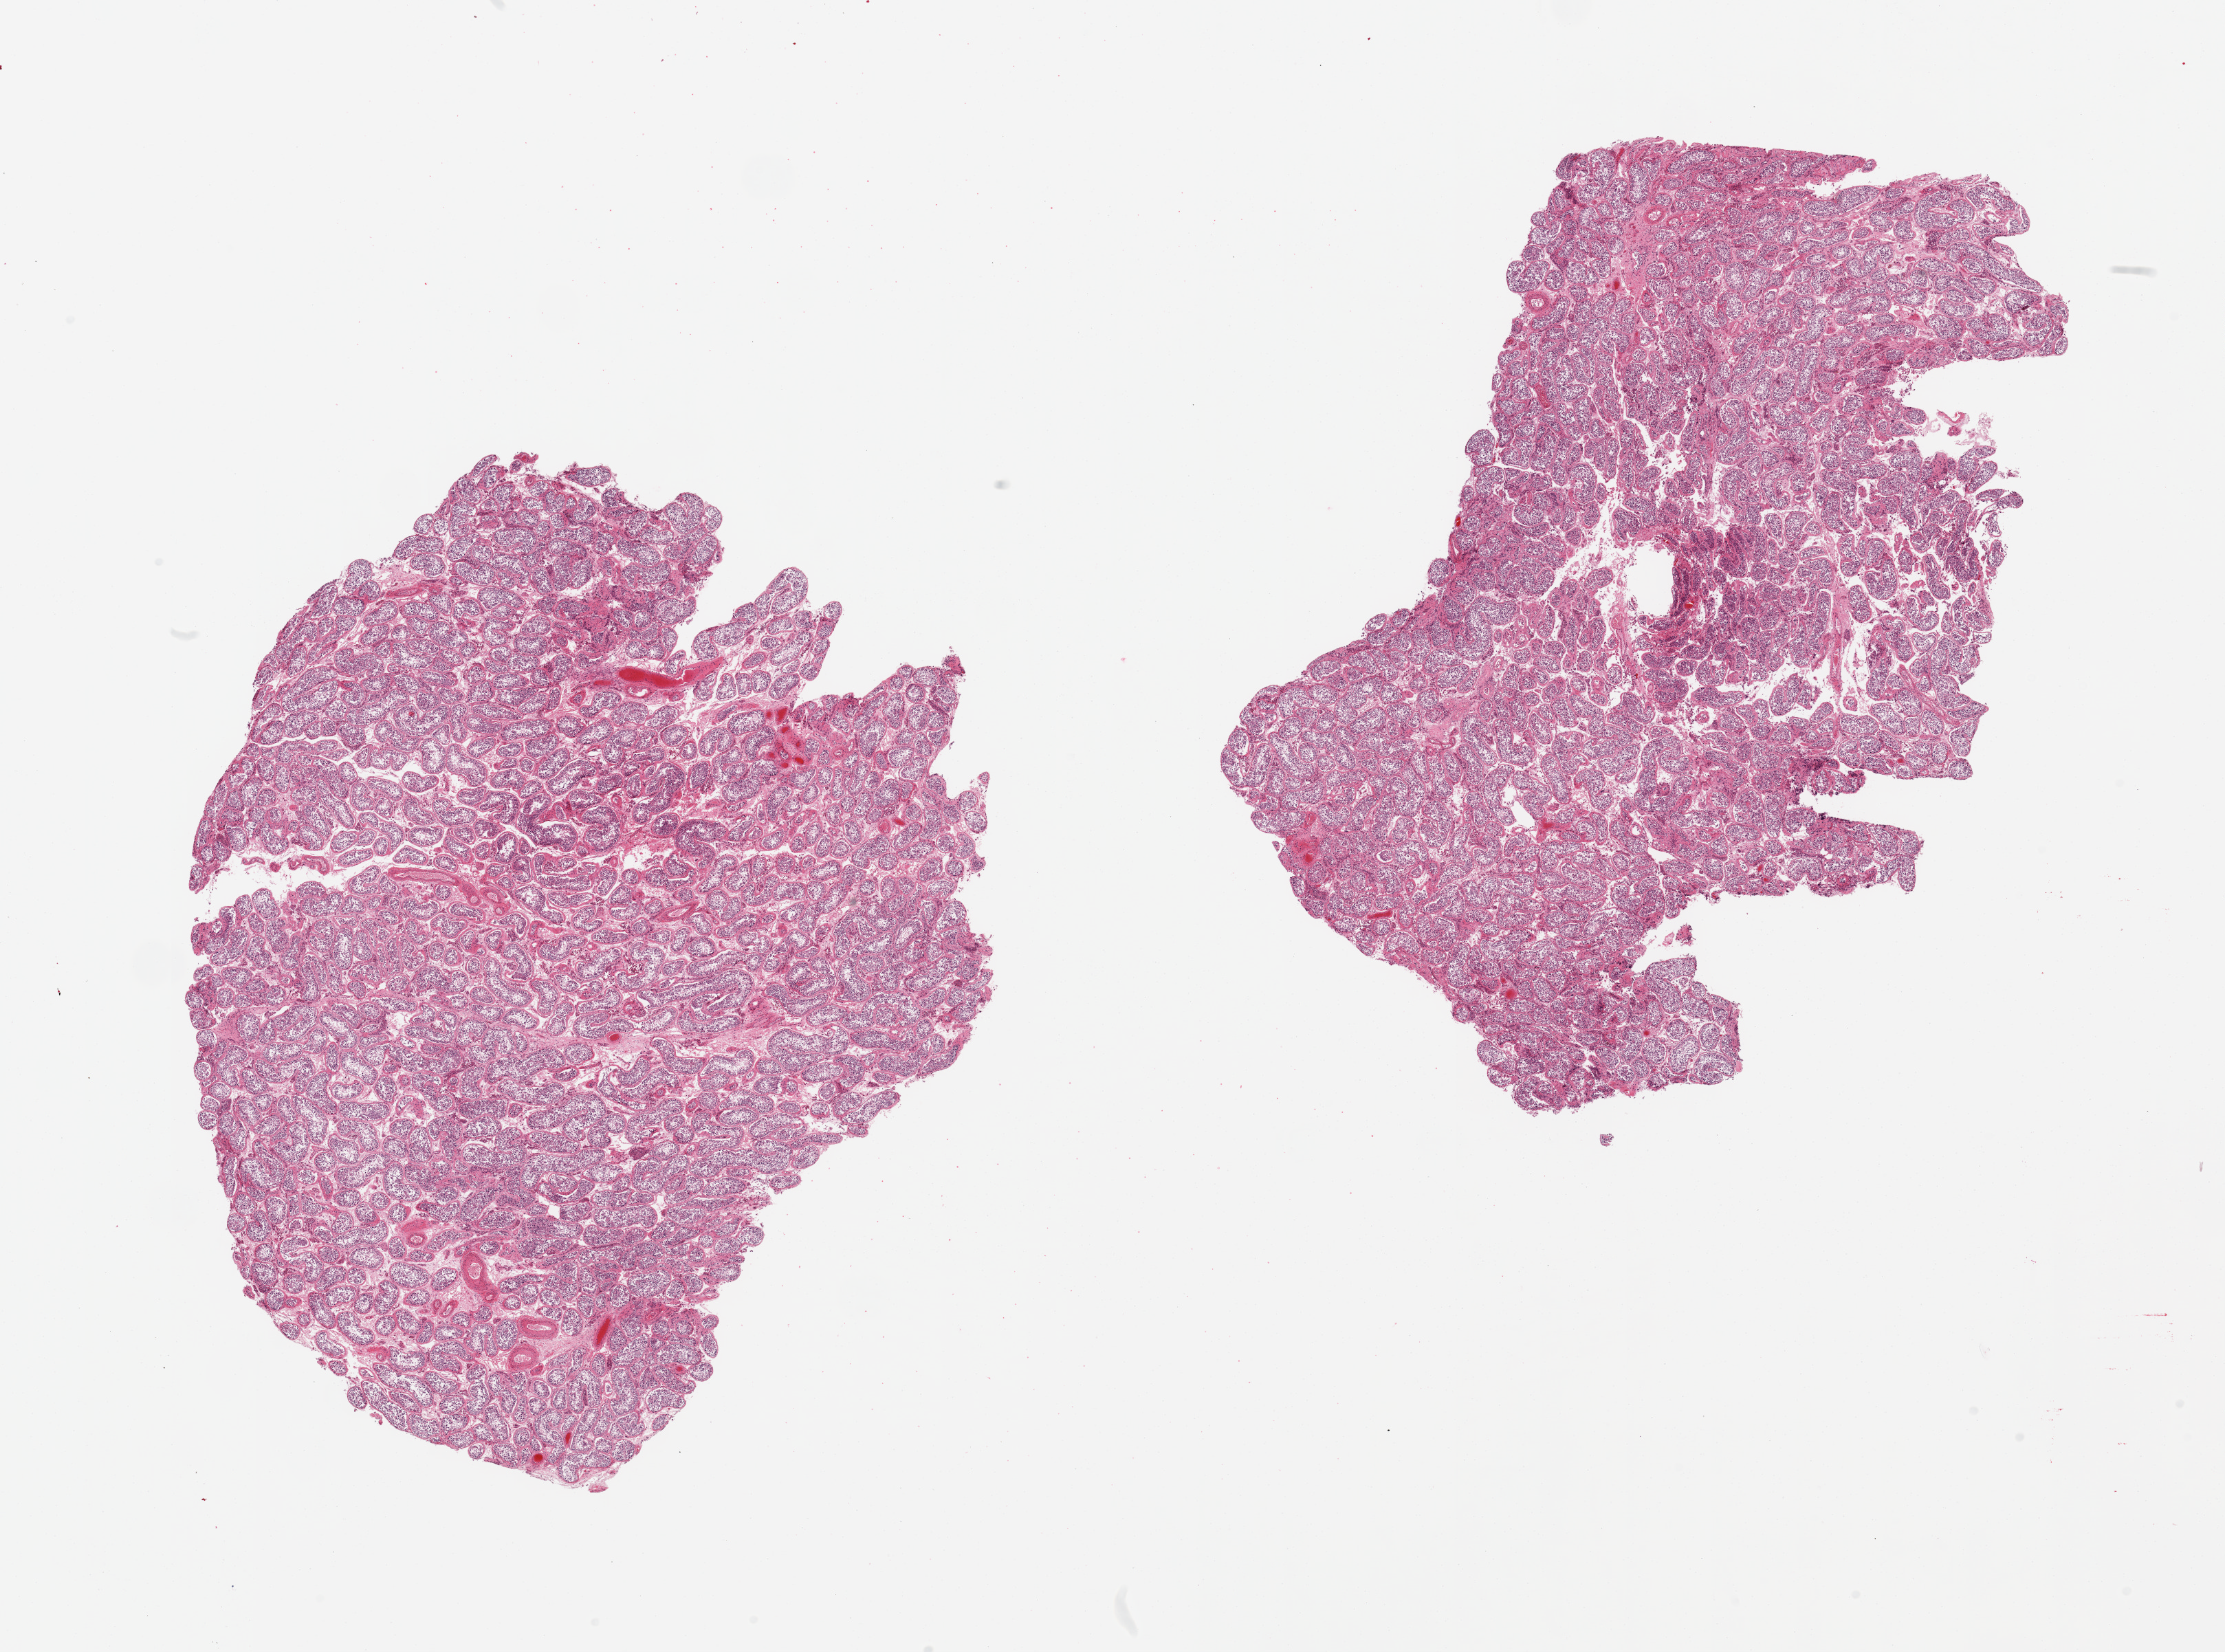
Digitized haematoxylin and eosin-stained section, brightfield — low-resolution overview of the scanned area, about 25.6 x 19.0 mm; PAXgene-fixed paraffin-embedded (PFPE) section; sampled site (target tissue): testis; donor tissue sample. Male donor.
Pathologist's review note for this sample: 2 pieces, spermatogenesisis present.